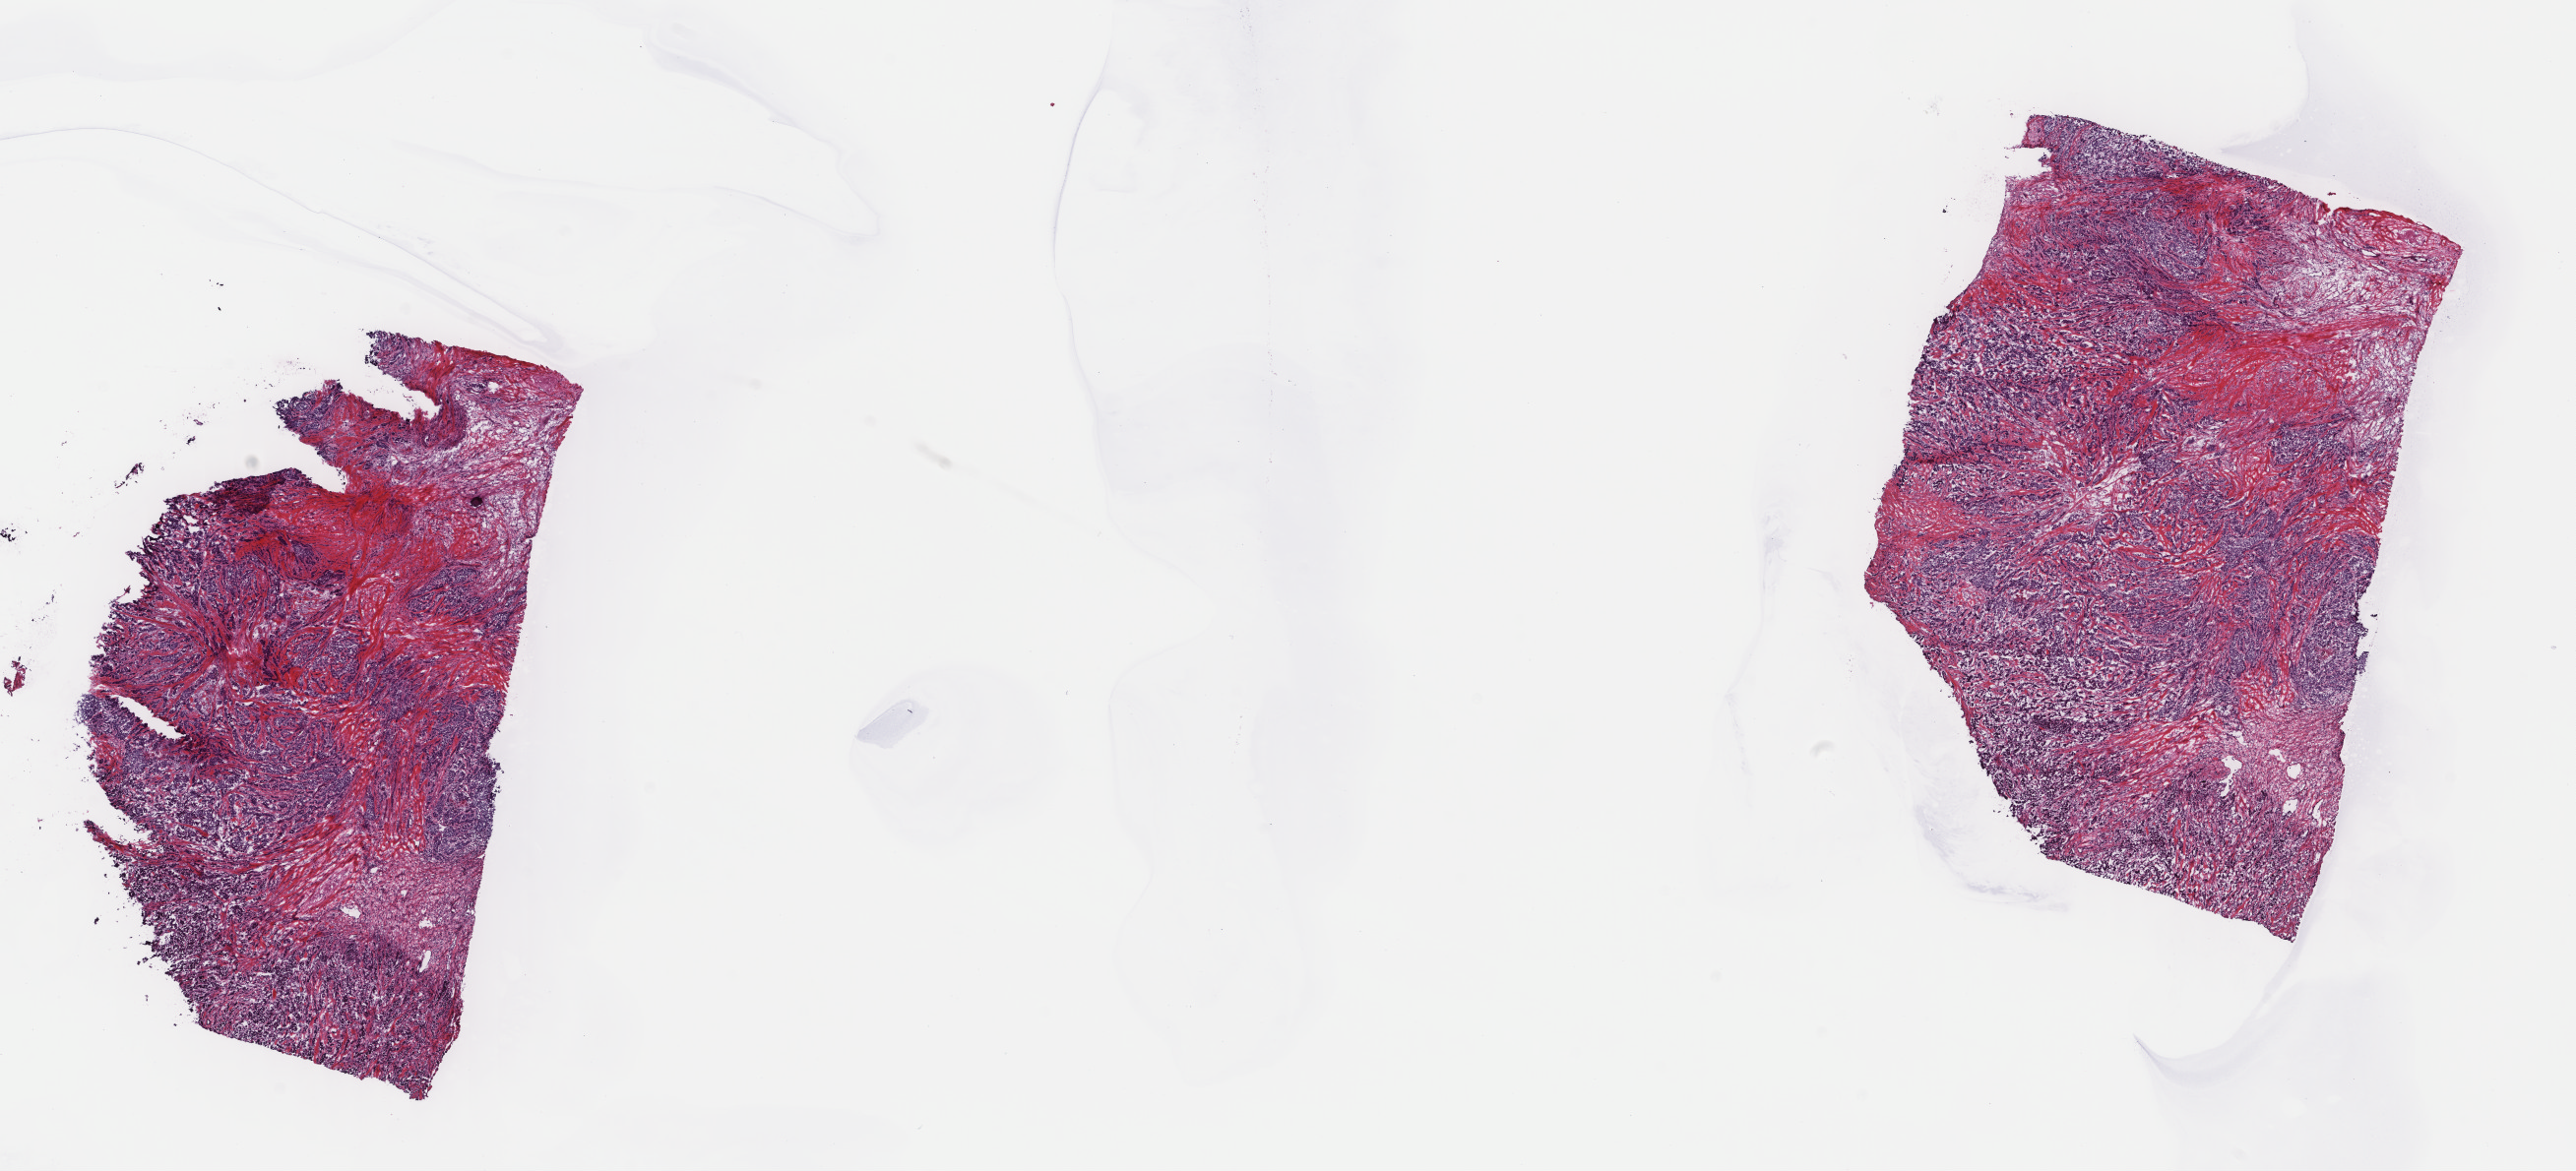
Digitized Hematoxylin and eosin (H&E) stained tissue section (whole slide) — shown as a low-resolution overview of the whole scanned area (about 20.8 x 9.4 mm). Frozen section. Sample: primary tumour, breast. Female, age 39 years at initial diagnosis. Slide review estimates, as recorded: tumour cells 75%, tumour nuclei 80%, normal cells 0%, stromal cells 25%, necrosis 0%. Inflammatory infiltration, as recorded: lymphocyte infiltration 2%, monocyte infiltration 0%, neutrophil infiltration 0%.
• AJCC pathologic stage: IIB (7th edition)
• pathologic diagnosis: Infiltrating duct carcinoma, NOS
• laterality: left
• TNM: T2 N1 M0